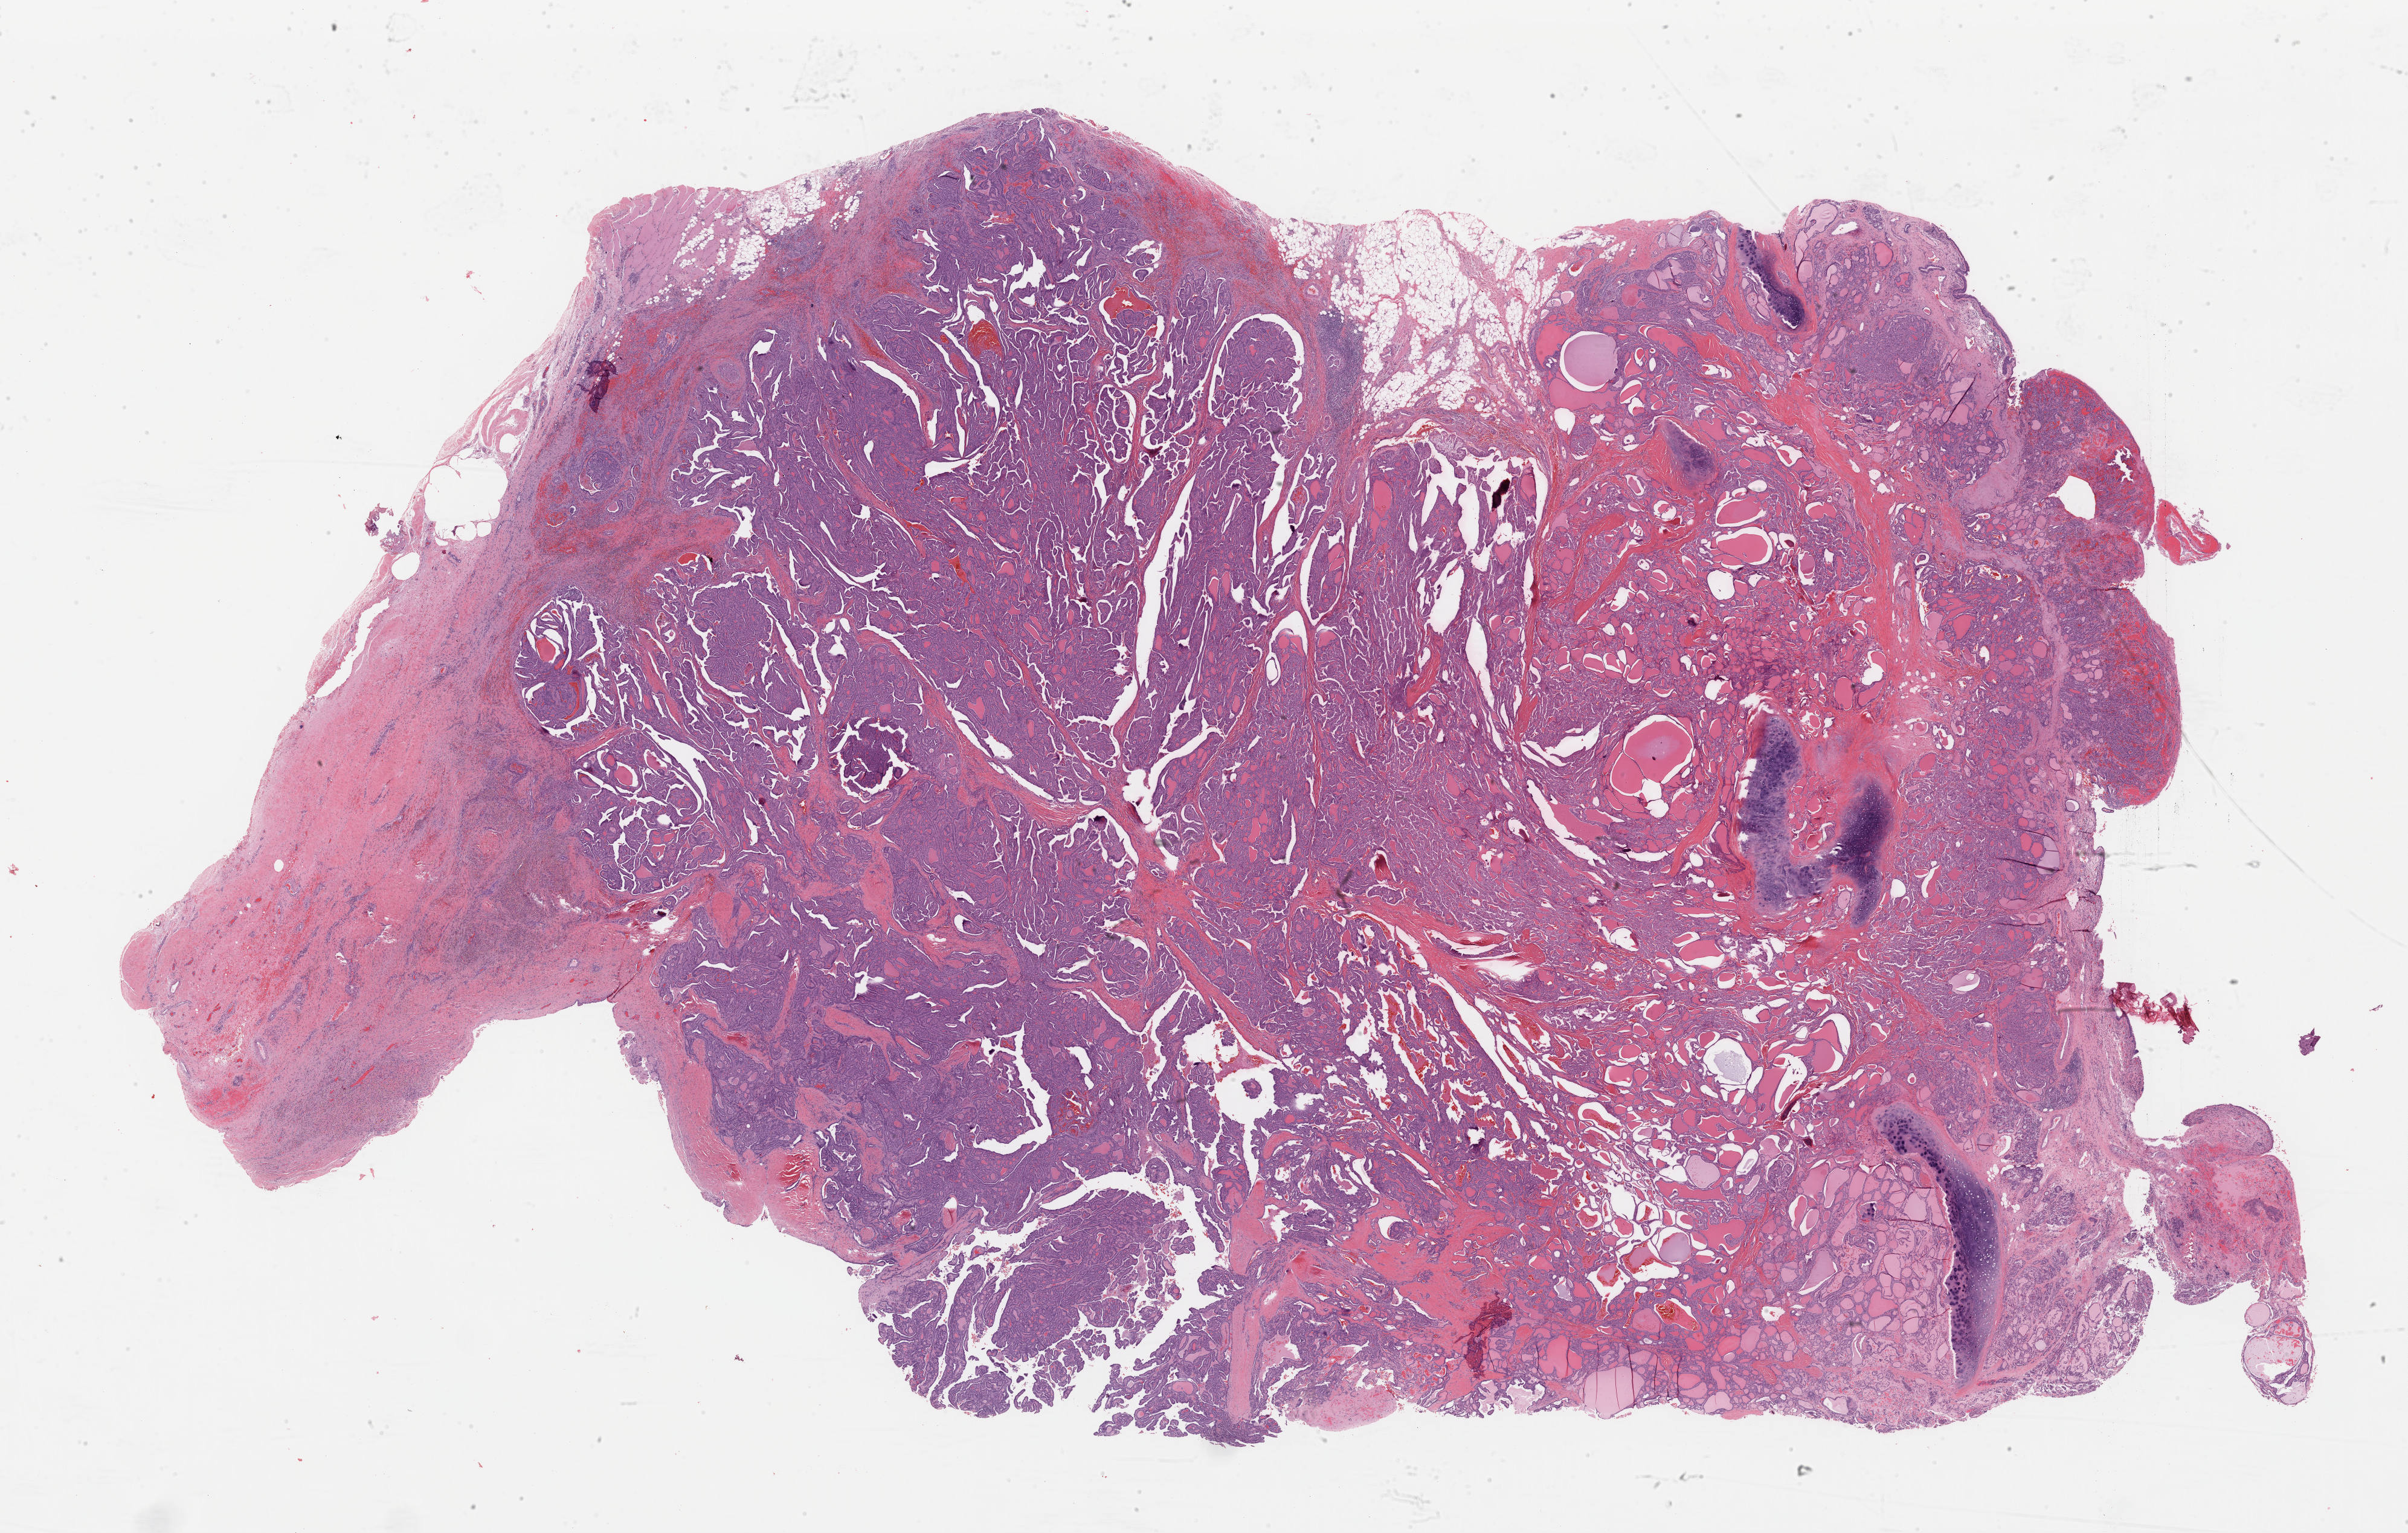
Whole-slide histology image, H&E-stained — shown as a low-resolution overview of the whole scanned area (about 31.5 x 20.0 mm); formalin-fixed paraffin-embedded (FFPE) diagnostic section; thyroid, primary tumour sample. Female patient; age at initial diagnosis 62 years.
Pathologic diagnosis: Papillary adenocarcinoma, NOS (thyroid gland).